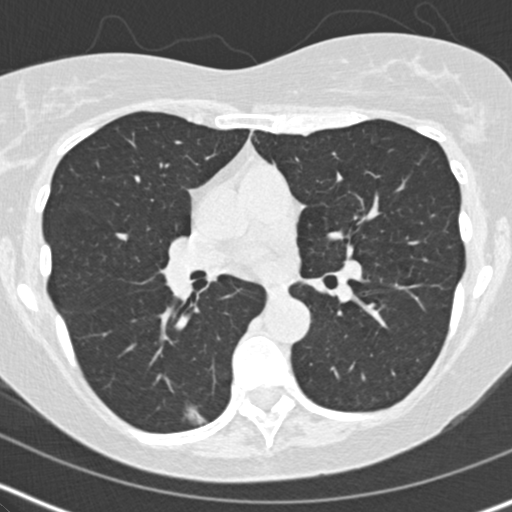
Axial slice from a low-dose chest CT screening exam, second screening round (one year after baseline), lung window (W 1500 / L -600 HU), 2 mm slice thickness, 120 kVp, 512 × 512 image matrix, field of view 304 × 304 mm. Female, age 60 years at enrolment.
Expert-annotated lung lesion, bounding box [x1, y1, x2, y2] px = [168, 391, 221, 436]. The screening reader recorded 2 non-calcified nodules or masses ≥4 mm on this exam (right middle lobe, right middle lobe); which of them this box marks is not recorded. Official screen result: positive, no significant change: stable abnormalities potentially related to lung cancer, unchanged since the prior screening exam. Lung cancer was diagnosed 453 days after this screen: acinar cell carcinoma, right lower lobe, moderately differentiated (G2), stage IA (AJCC 6th edition), 10 mm at pathology.